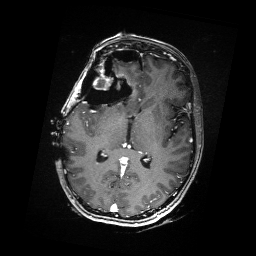
Brain MRI from a brain-tumour surgery series, one axial slice. Slice 90 of 176 in the series (ordered by position). T1-weighted post-contrast. 256 × 256 image matrix. From the clinical record (not read from this slice): histopathology: Metastatic Carcinoma from Breast primary; tumour location: Right Frontal.
Outlined on this slice (outlined manually by an expert reader):
- residual tumour: bounding box [x1, y1, x2, y2] px = [91, 69, 112, 88]